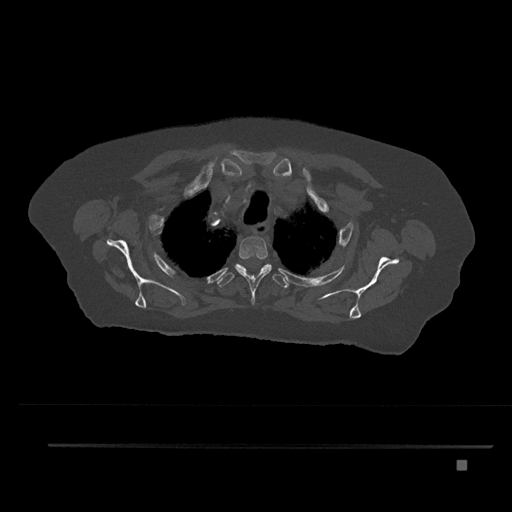
CT including the spine, one axial slice. Slice 657 of 797 in the series (ordered by position). Reconstruction kernel Br40s/3. Bone window (W 1800 / L 400 HU). 0.5 mm slice thickness. 512 × 512 image matrix, field of view 437 × 437 mm. Patient: female, 76 years. From the clinical record (not read from this slice): primary cancer: lung.
Outlined on this slice (semi-automatically segmented with operator editing):
- T2 vertebra: bounding box [x1, y1, x2, y2] px = [235, 231, 272, 304]
- T3 vertebra: [217, 263, 288, 288]